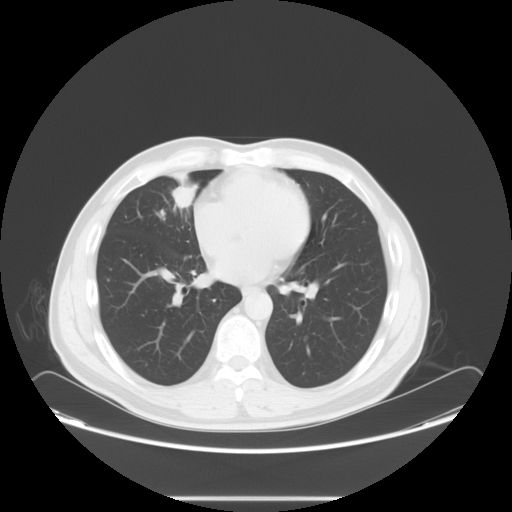
Chest CT, one axial slice. Position 35 of 73 along the scan axis. 120 kVp. Lung window (W 1500 / L -600 HU). 5 mm slice thickness. 512 × 512 image matrix, field of view 429 × 429 mm. Male patient, age 47 years. Case-level facts recorded for this patient, not image findings: clinical TNM (as recorded): T1c N3 M0.
Outlined on this slice (rectangle marked by the reading radiologist):
- lung tumour (recorded histology: adenocarcinoma): box from (x=153, y=174) to (x=198, y=220) px